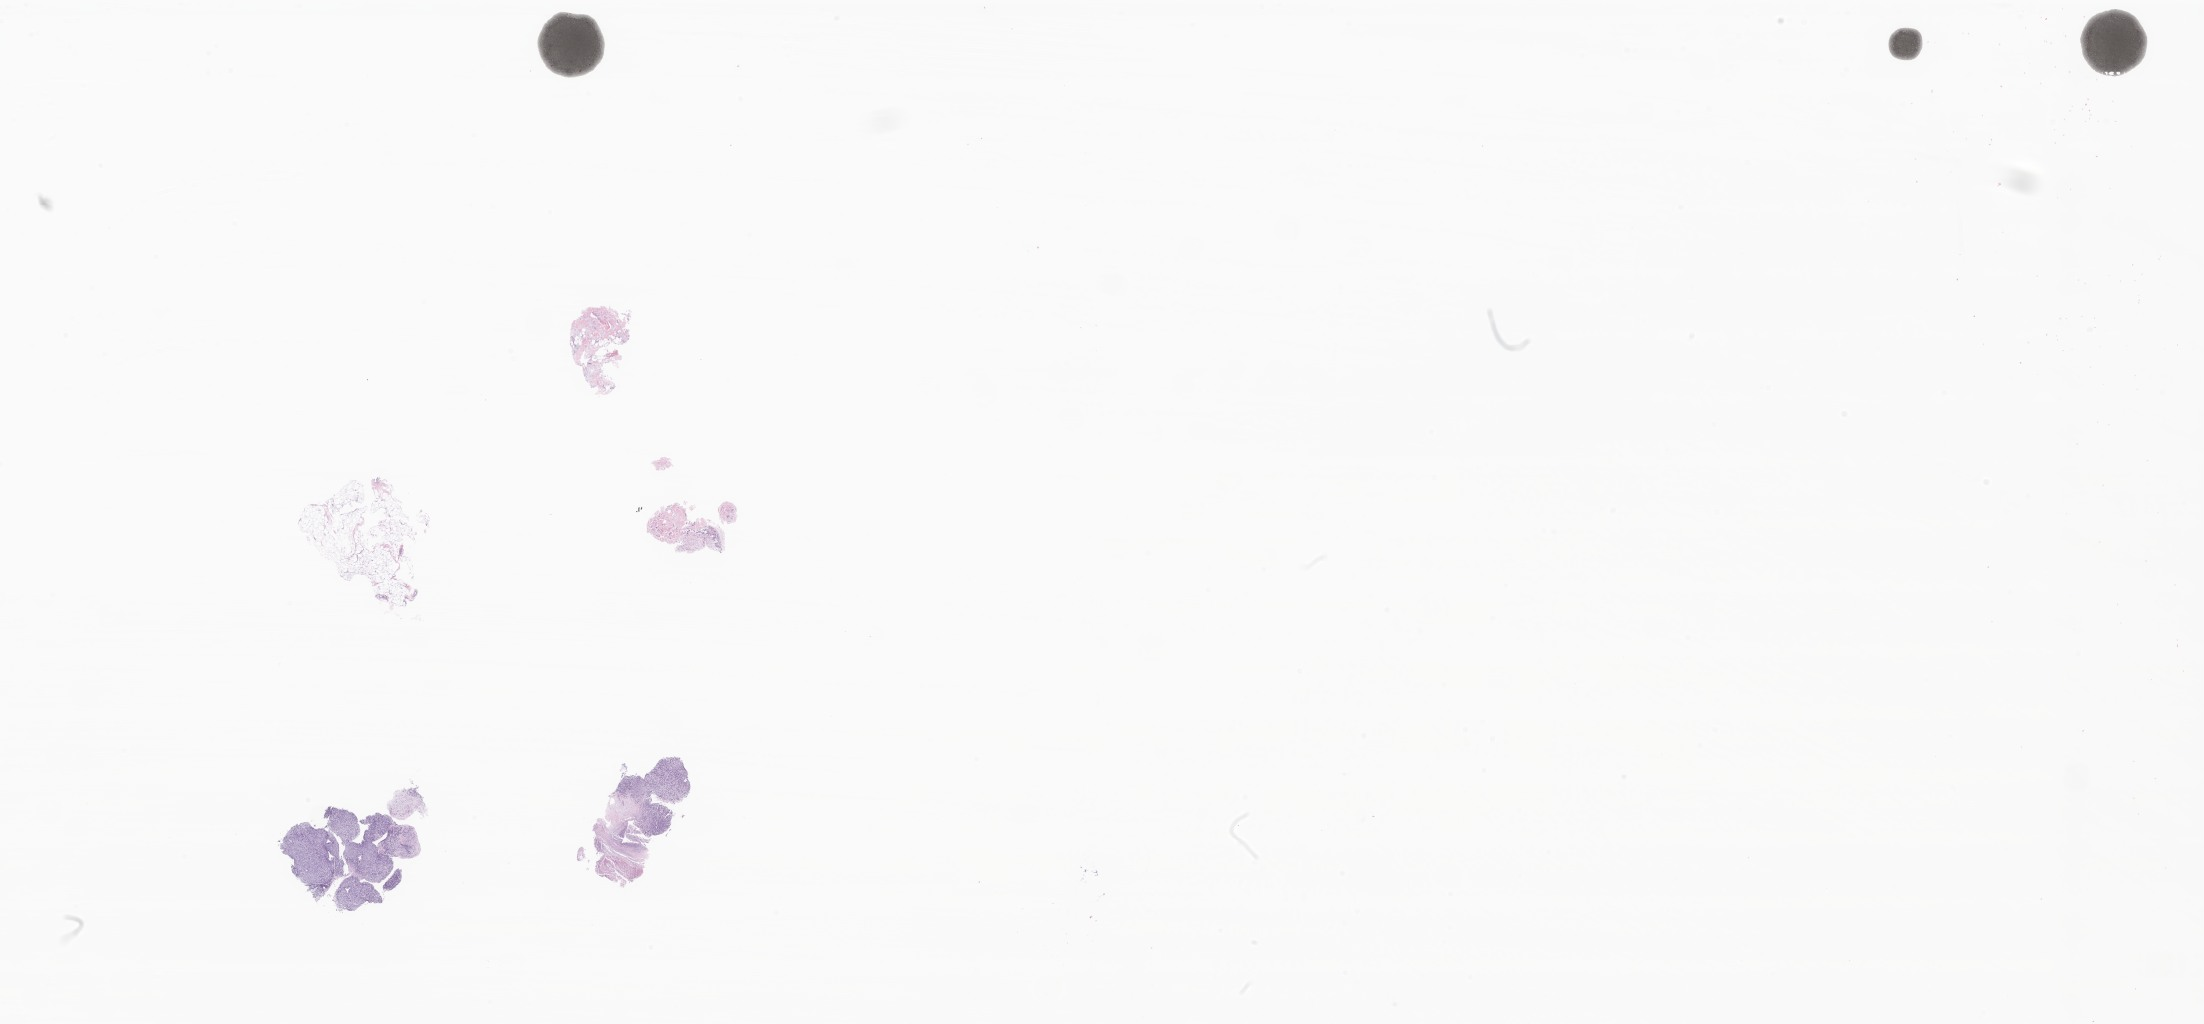
Haematoxylin and eosin whole-slide image of tumor tissue from the upper limb lymph node, a low-resolution overview of the entire scanned area, about 37.2 x 17.3 mm. Formalin-fixed paraffin-embedded section. Patient: male, age 226 months (18 years 10 months).
Diagnosis: Spindle cell sarcoma.